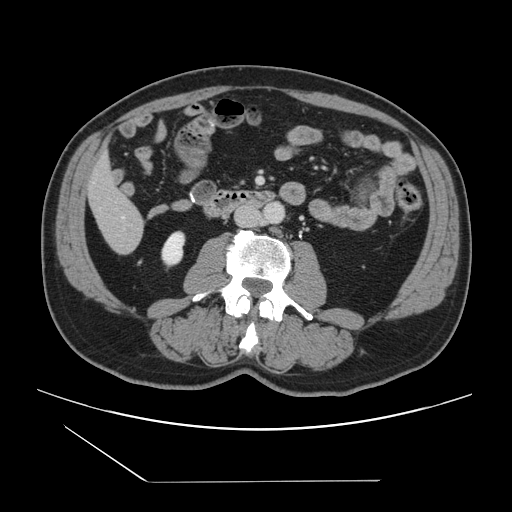
Contrast-enhanced abdominal CT, one axial slice; slice 25 of 157 in the series (ordered by position); intravenous contrast given; soft-tissue window (W 400 / L 40 HU); 2.5 mm slice thickness; 512 × 512 image matrix, field of view 407 × 407 mm. Male patient, age 61 years. From the clinical record (not read from this slice): diagnosis: colorectal cancer liver metastases, imaged before liver resection; multiple liver metastases: yes.
Outlined on this slice (manually delineated by an expert):
- liver: bounding box <90,159,144,253> (left, top, right, bottom; pixels)
- planned liver remnant (the part of the liver to remain after resection): <90,158,135,218>